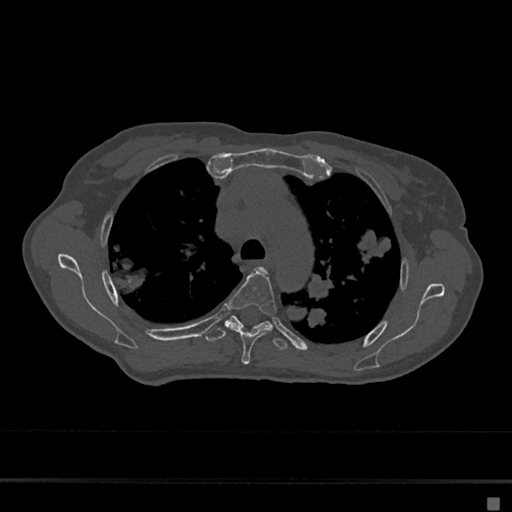
CT including the spine, one axial slice; slice 489 of 797 in the series (ordered by position); reconstruction kernel Br40s/3; 120 kVp; bone window (W 1800 / L 400 HU); 512 × 512 image matrix. Patient: female, 68 years. Case-level facts recorded for this patient, not image findings: primary cancer: renal.
Annotated regions visible in this slice (semi-automatic segmentation, software-assisted and operator-edited):
- T4 vertebra: bounding box (x1, y1, x2, y2) in pixels: (228, 267, 277, 365)
- T5 vertebra: (206, 315, 288, 351)